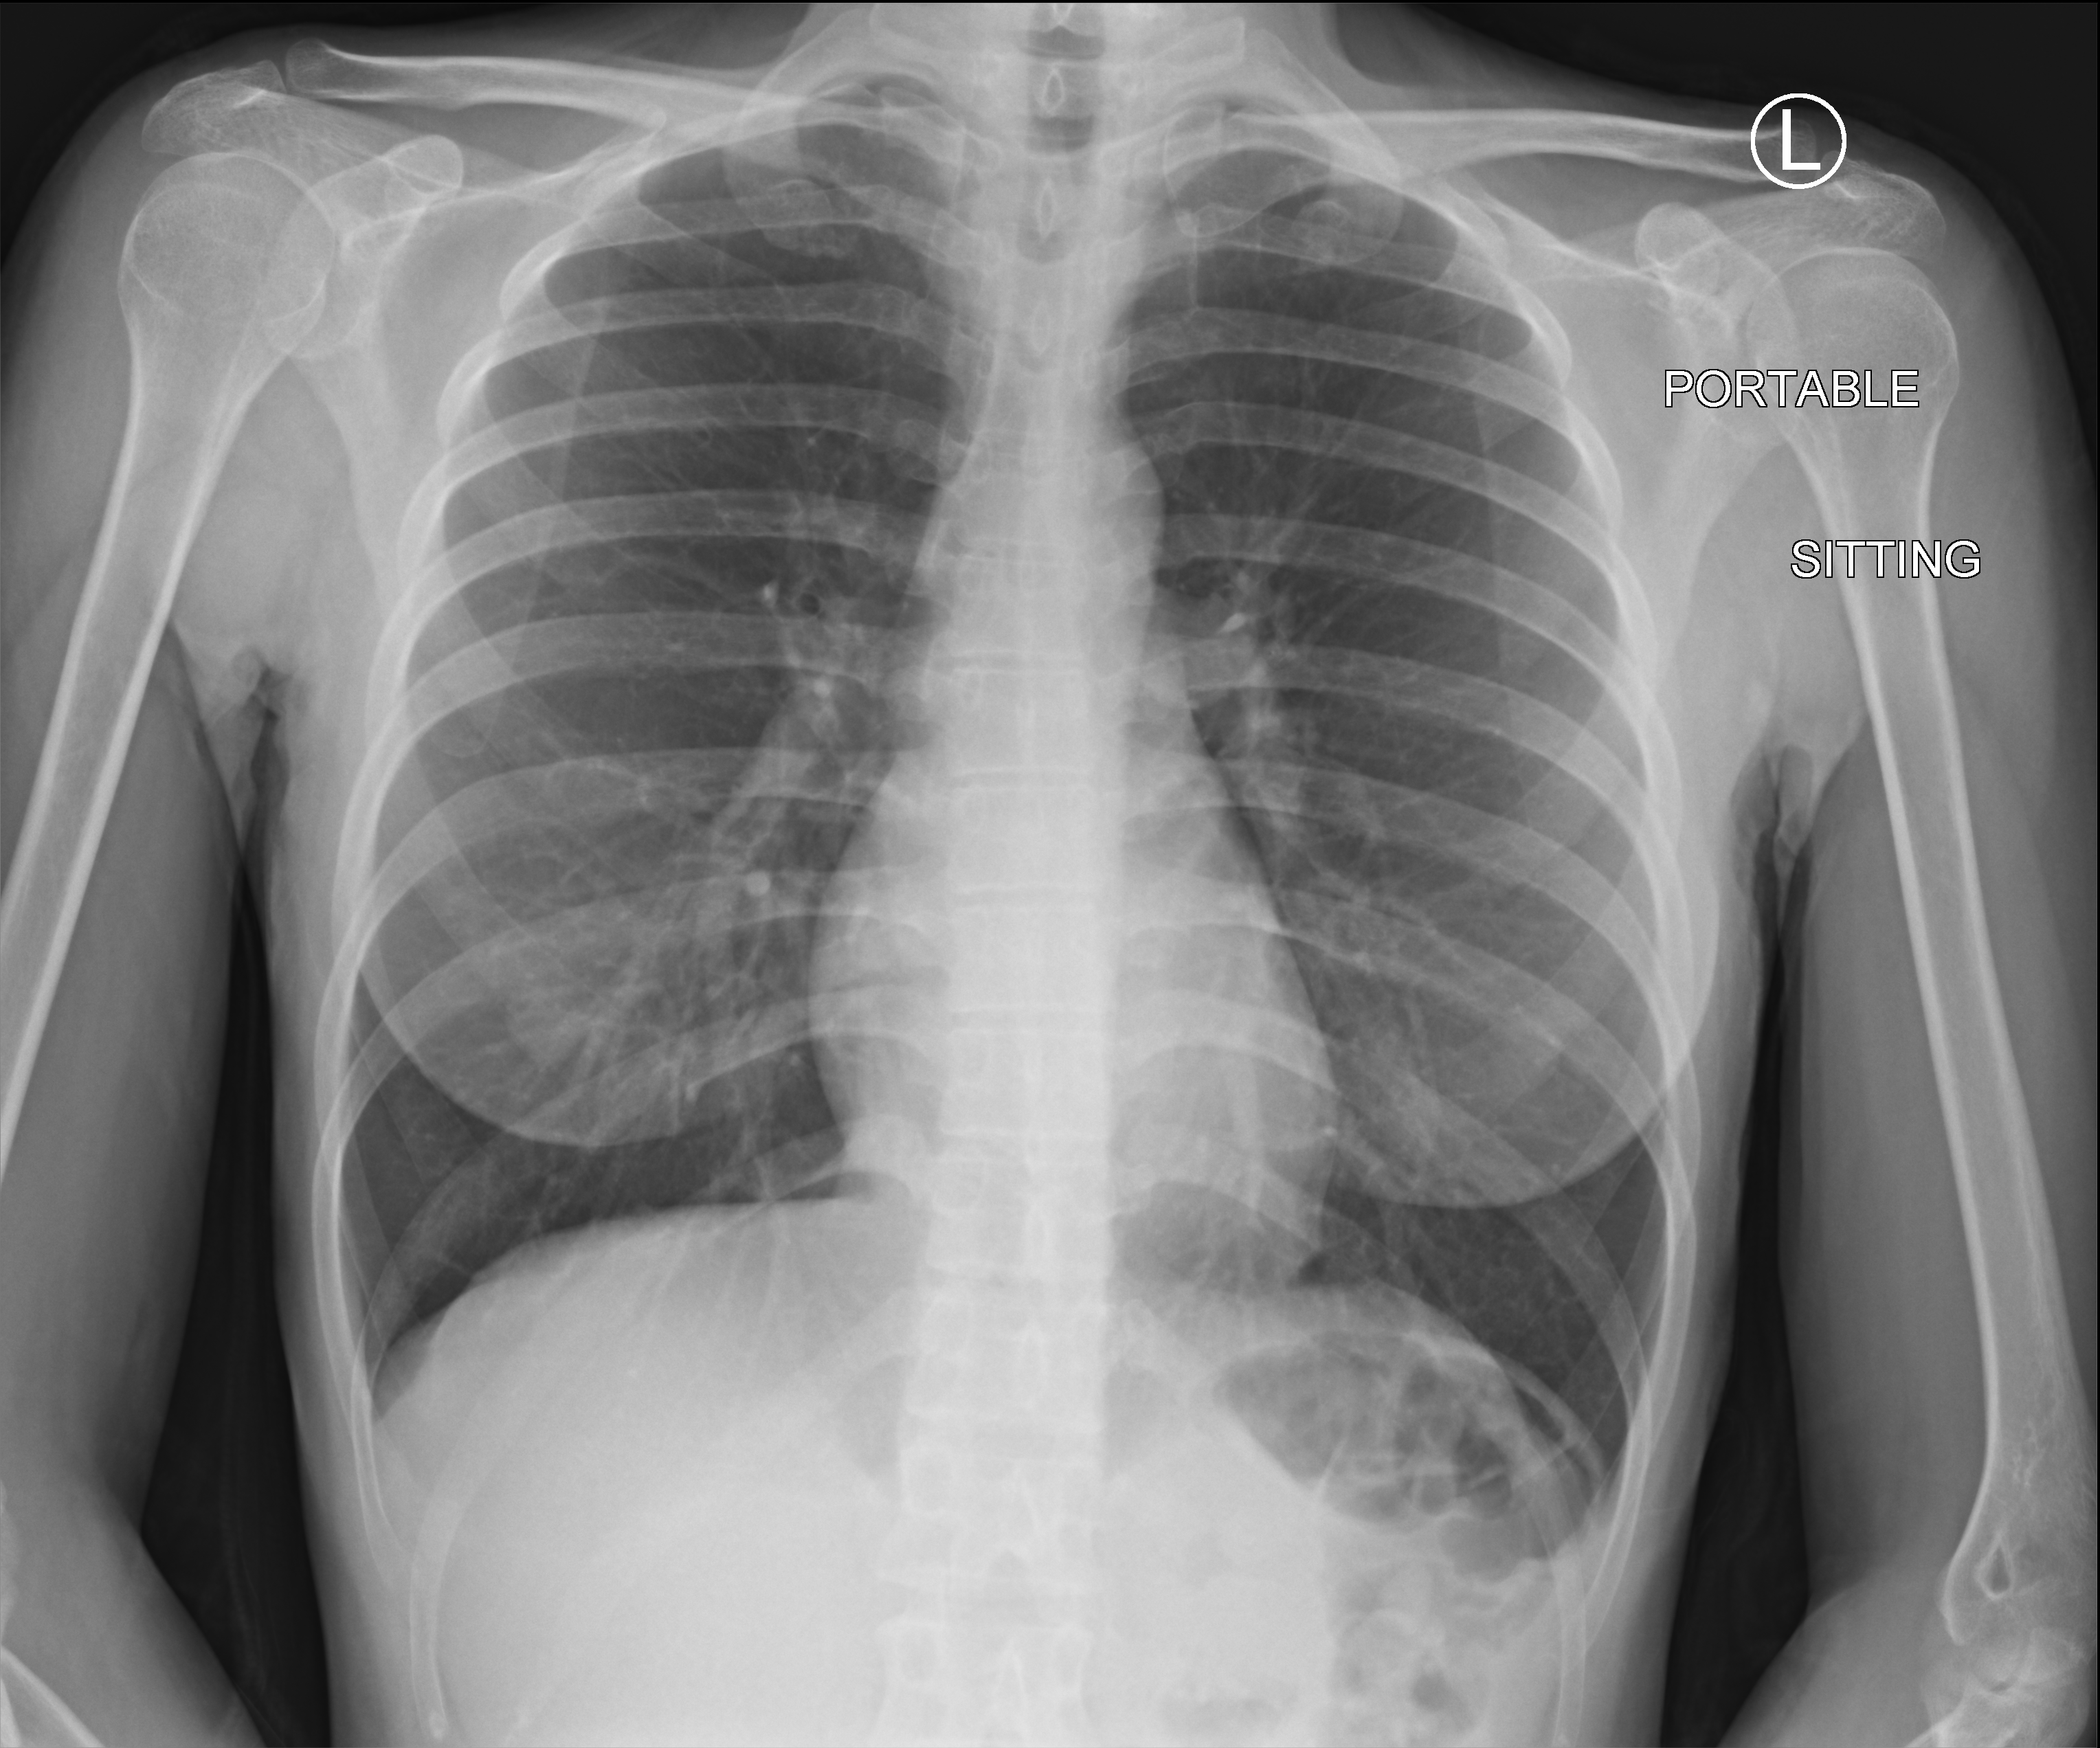
Bedside chest radiograph (computed radiography). Patient hospitalised with COVID-19; female, aged 18–59 years.
From the hospital-stay record, not from the radiograph (when in the stay this image was taken is not recorded):
- admitted to intensive care during this hospital stay: no